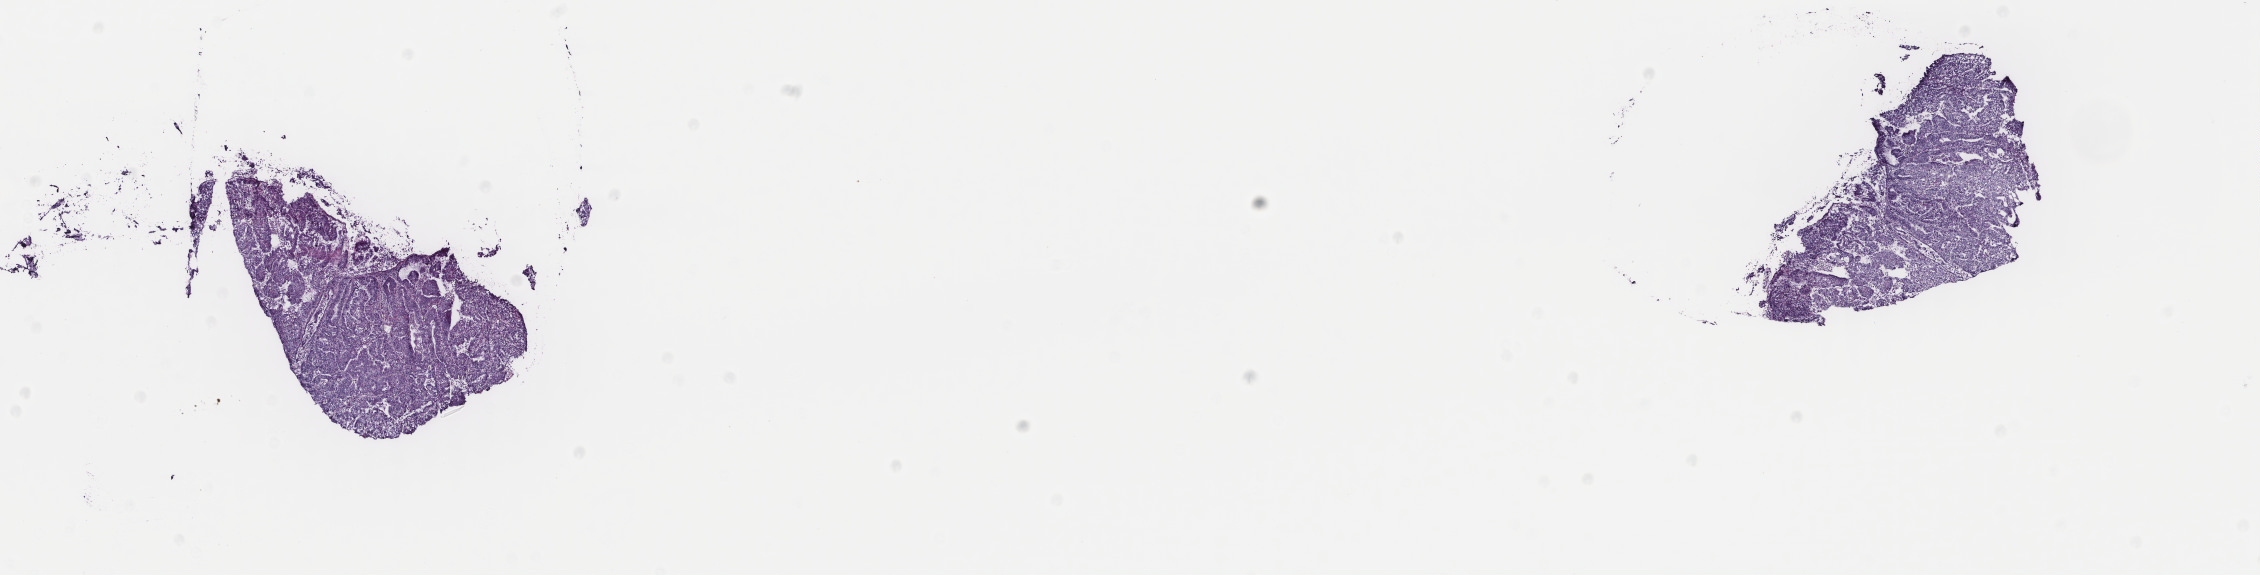
Digitized Hematoxylin and eosin (H&E) stained tissue section (whole slide) — a low-resolution overview of the entire scanned area, about 17.9 x 4.6 mm, frozen section from the top of the tissue portion, uterus, primary tumour sample. Patient: female, age at initial diagnosis 54 years.
Pathologic diagnosis: Endometrioid adenocarcinoma, NOS (endometrium).